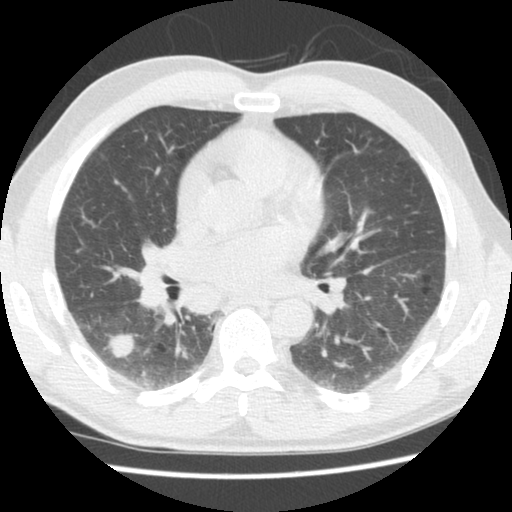
Low-dose screening chest CT, axial slice, second screening round (one year after baseline), lung window (W 1500 / L -600 HU), standard (soft-tissue) reconstruction kernel (STANDARD), 512 × 512 image matrix. Male participant, aged 60 years at enrolment.
Expert-annotated lung lesion, bounding box <90,321,143,372> (left, top, right, bottom; pixels). Reader record for this screening exam (exam-level; its link to the box is not recorded): non-calcified nodule or mass ≥4 mm, right lower lobe, 17 × 15 mm, poorly defined margins, soft tissue attenuation, pre-existing on the prior screen: yes; interval growth: yes. Official screen result: positive, other. Later outcome: lung cancer diagnosed 44 days after this screen — adenocarcinoma, NOS, right lower lobe, stage IA (AJCC 6th edition), 18 mm at pathology.